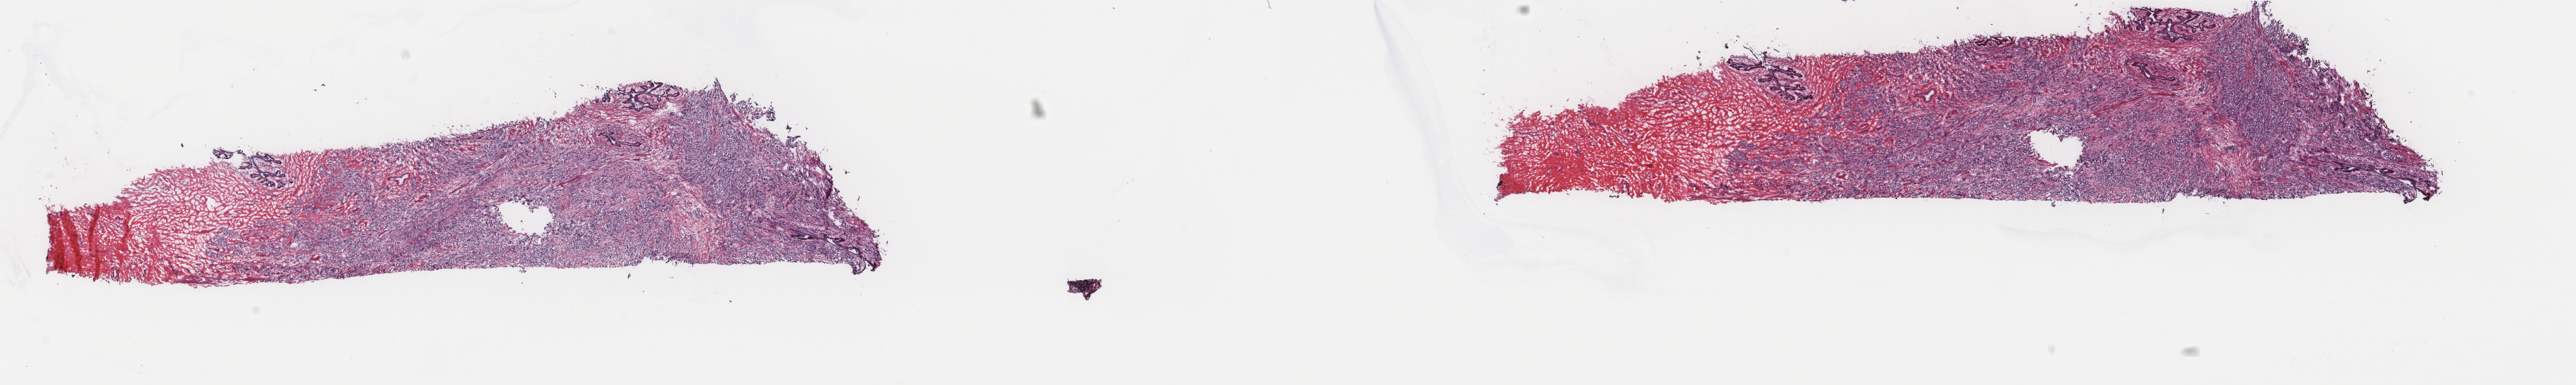
Hematoxylin and eosin (H&E) stained whole-slide image, low-resolution overview of the scanned area, about 29.0 x 4.3 mm; frozen section from the top of the tissue portion; sample: primary tumour, breast. Female patient; age at initial diagnosis 42 years. Composition of this section per pathologist review: tumour cells 70%, tumour nuclei 75%, normal cells 30%, stromal cells 0%, necrosis 0%. Infiltration values recorded for this section: lymphocyte infiltration 0%, monocyte infiltration 0%, neutrophil infiltration 0%.
Laterality: right. Lymph nodes positive (case pathology): 3 of 18 examined. Diagnosis: Infiltrating duct carcinoma, NOS. AJCC pathologic stage: IIB. TNM: T2 N1a M0.